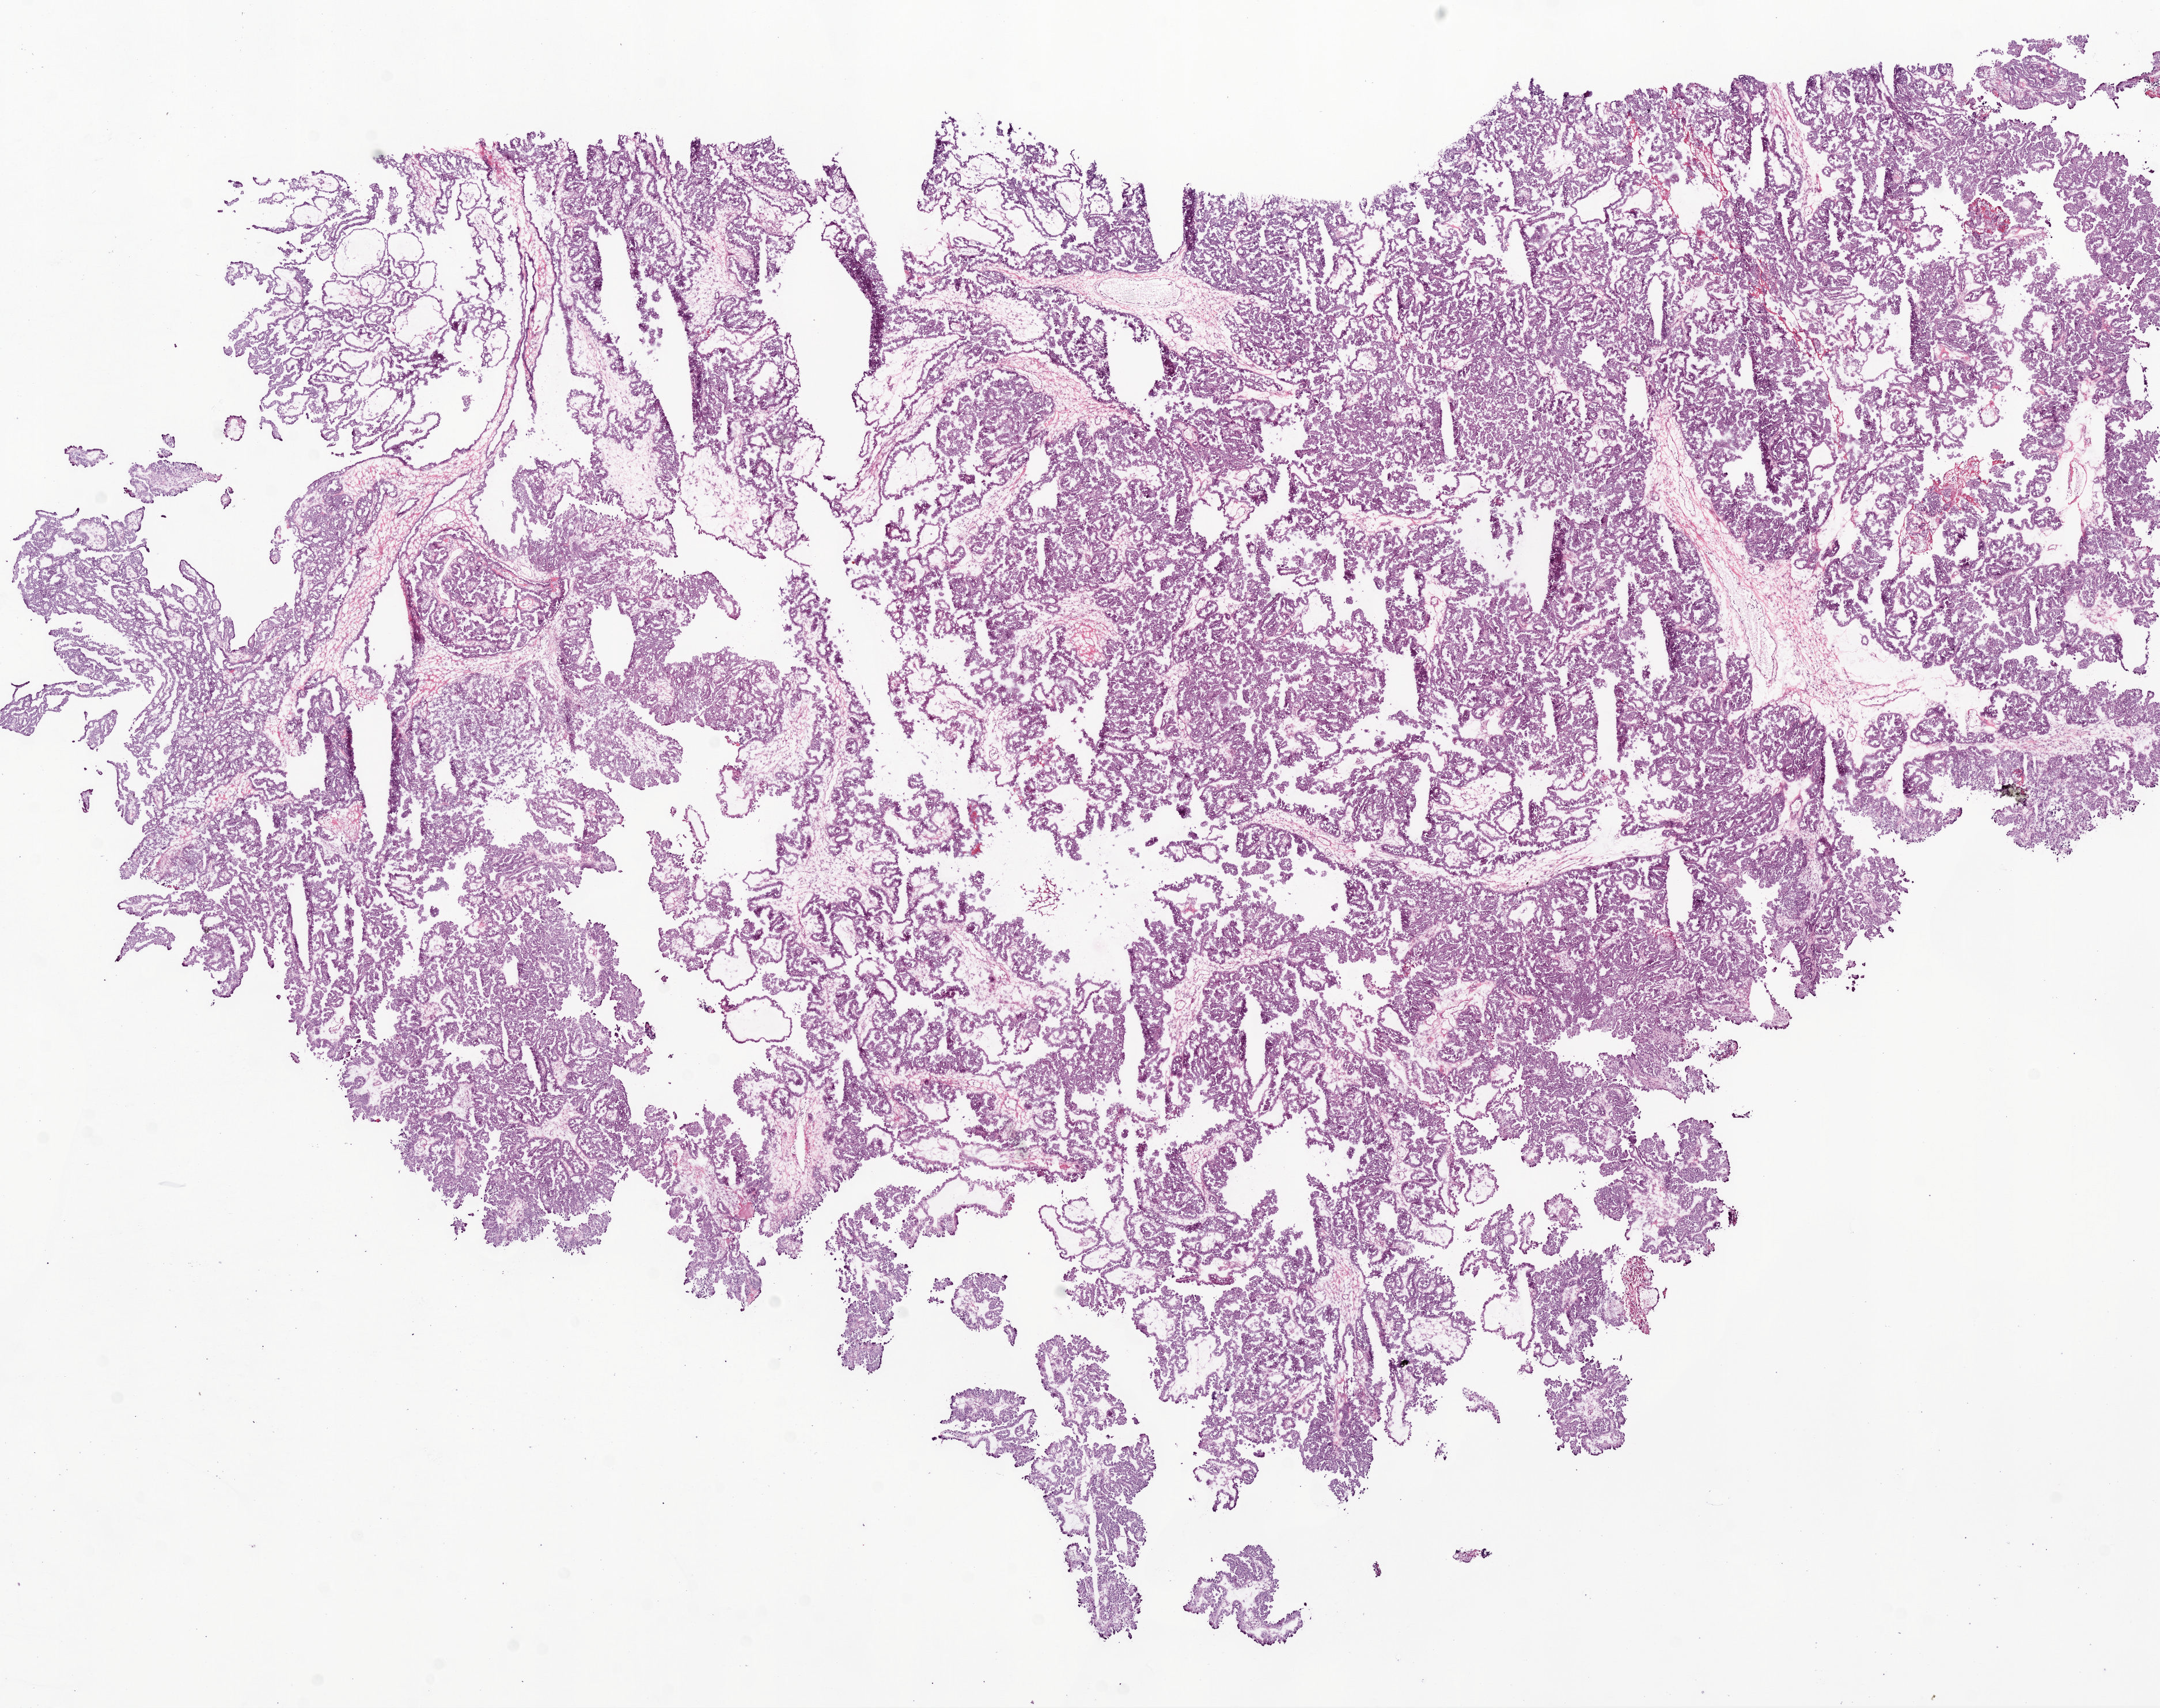
Digitized H&E tissue section (whole slide) — low-resolution overview of the scanned area, about 15.0 x 11.9 mm; frozen section from the bottom of the tissue portion; primary tumour sample from the ovary. Female patient; age at initial diagnosis 68 years. Histologic grade: G3 (poorly differentiated). Slide review estimates, as recorded: tumour cells 94%, tumour nuclei 95%, normal cells 0%, stromal cells 5%, necrosis 1%.
* diagnosis: Serous cystadenocarcinoma, NOS
* FIGO stage: IV